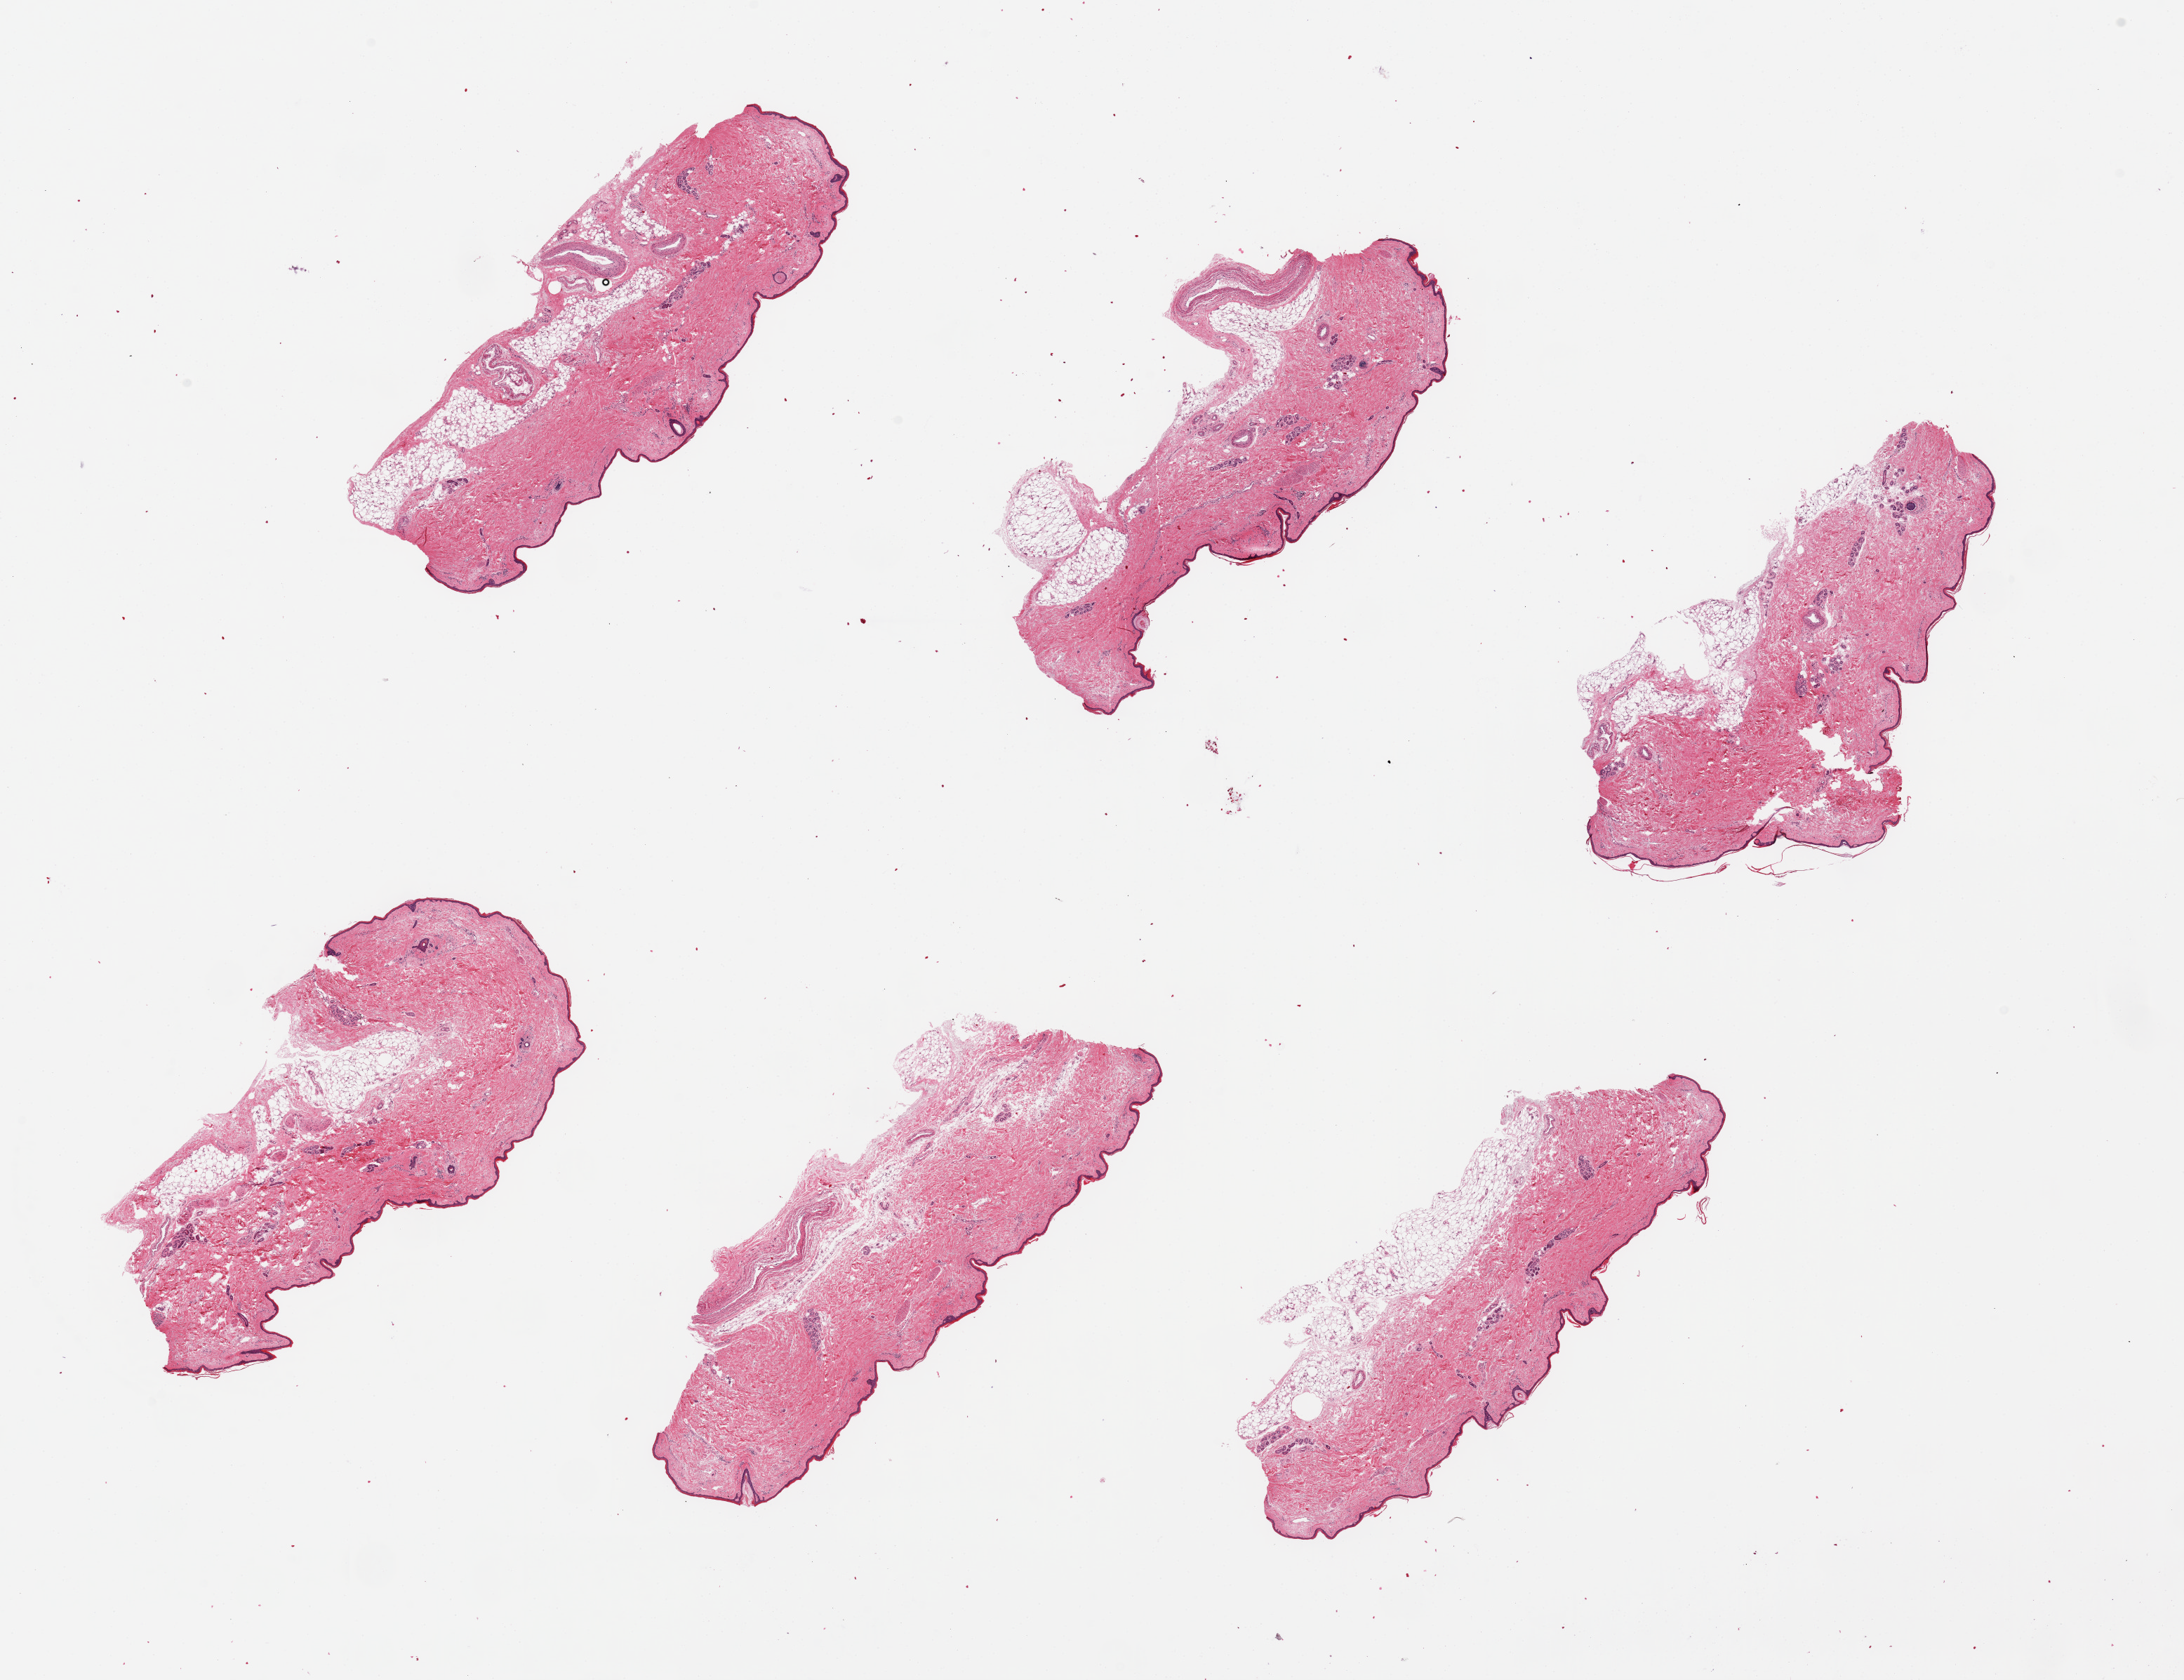
Whole-slide image, haematoxylin and eosin stain — a low-resolution overview of the entire scanned area, about 24.6 x 18.9 mm (acquisition: 20x scan), PAXgene-fixed paraffin-embedded (PFPE) section, section of skin of lower leg (target tissue), donor tissue sample.
Review note (as recorded): 6 pieces up to 6.5x3mm; squamous mucosa markedly atrophic, <1% of thickness.